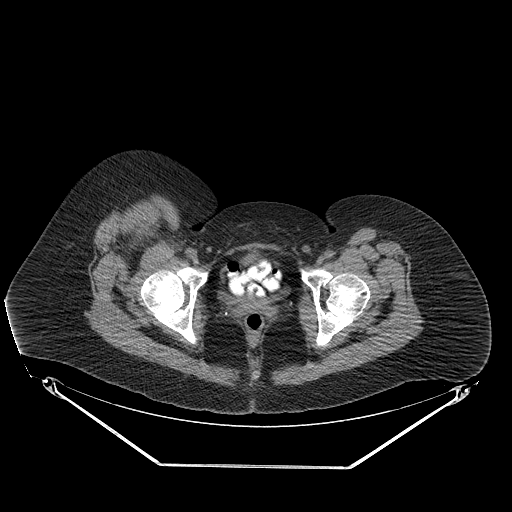
CT of an extremity soft-tissue mass (from a PET/CT study), one axial slice; slice 68 of 267 in the series (ordered by position); reconstruction kernel STANDARD; soft-tissue window (W 400 / L 40 HU); 3.75 mm slice thickness; 512 × 512 image matrix, field of view 500 × 500 mm. Female patient. From the clinical record (not read from this slice): histological type: malignant solitary fibrous tumor; grade: intermediate; site of the primary tumour: right thigh.
Annotated regions visible in this slice (expert contour drawn on MRI and transferred to this co-registered scan by the dataset authors):
- gross tumour volume including surrounding oedema: bounding box (x1, y1, x2, y2) in pixels: (110, 214, 165, 243)